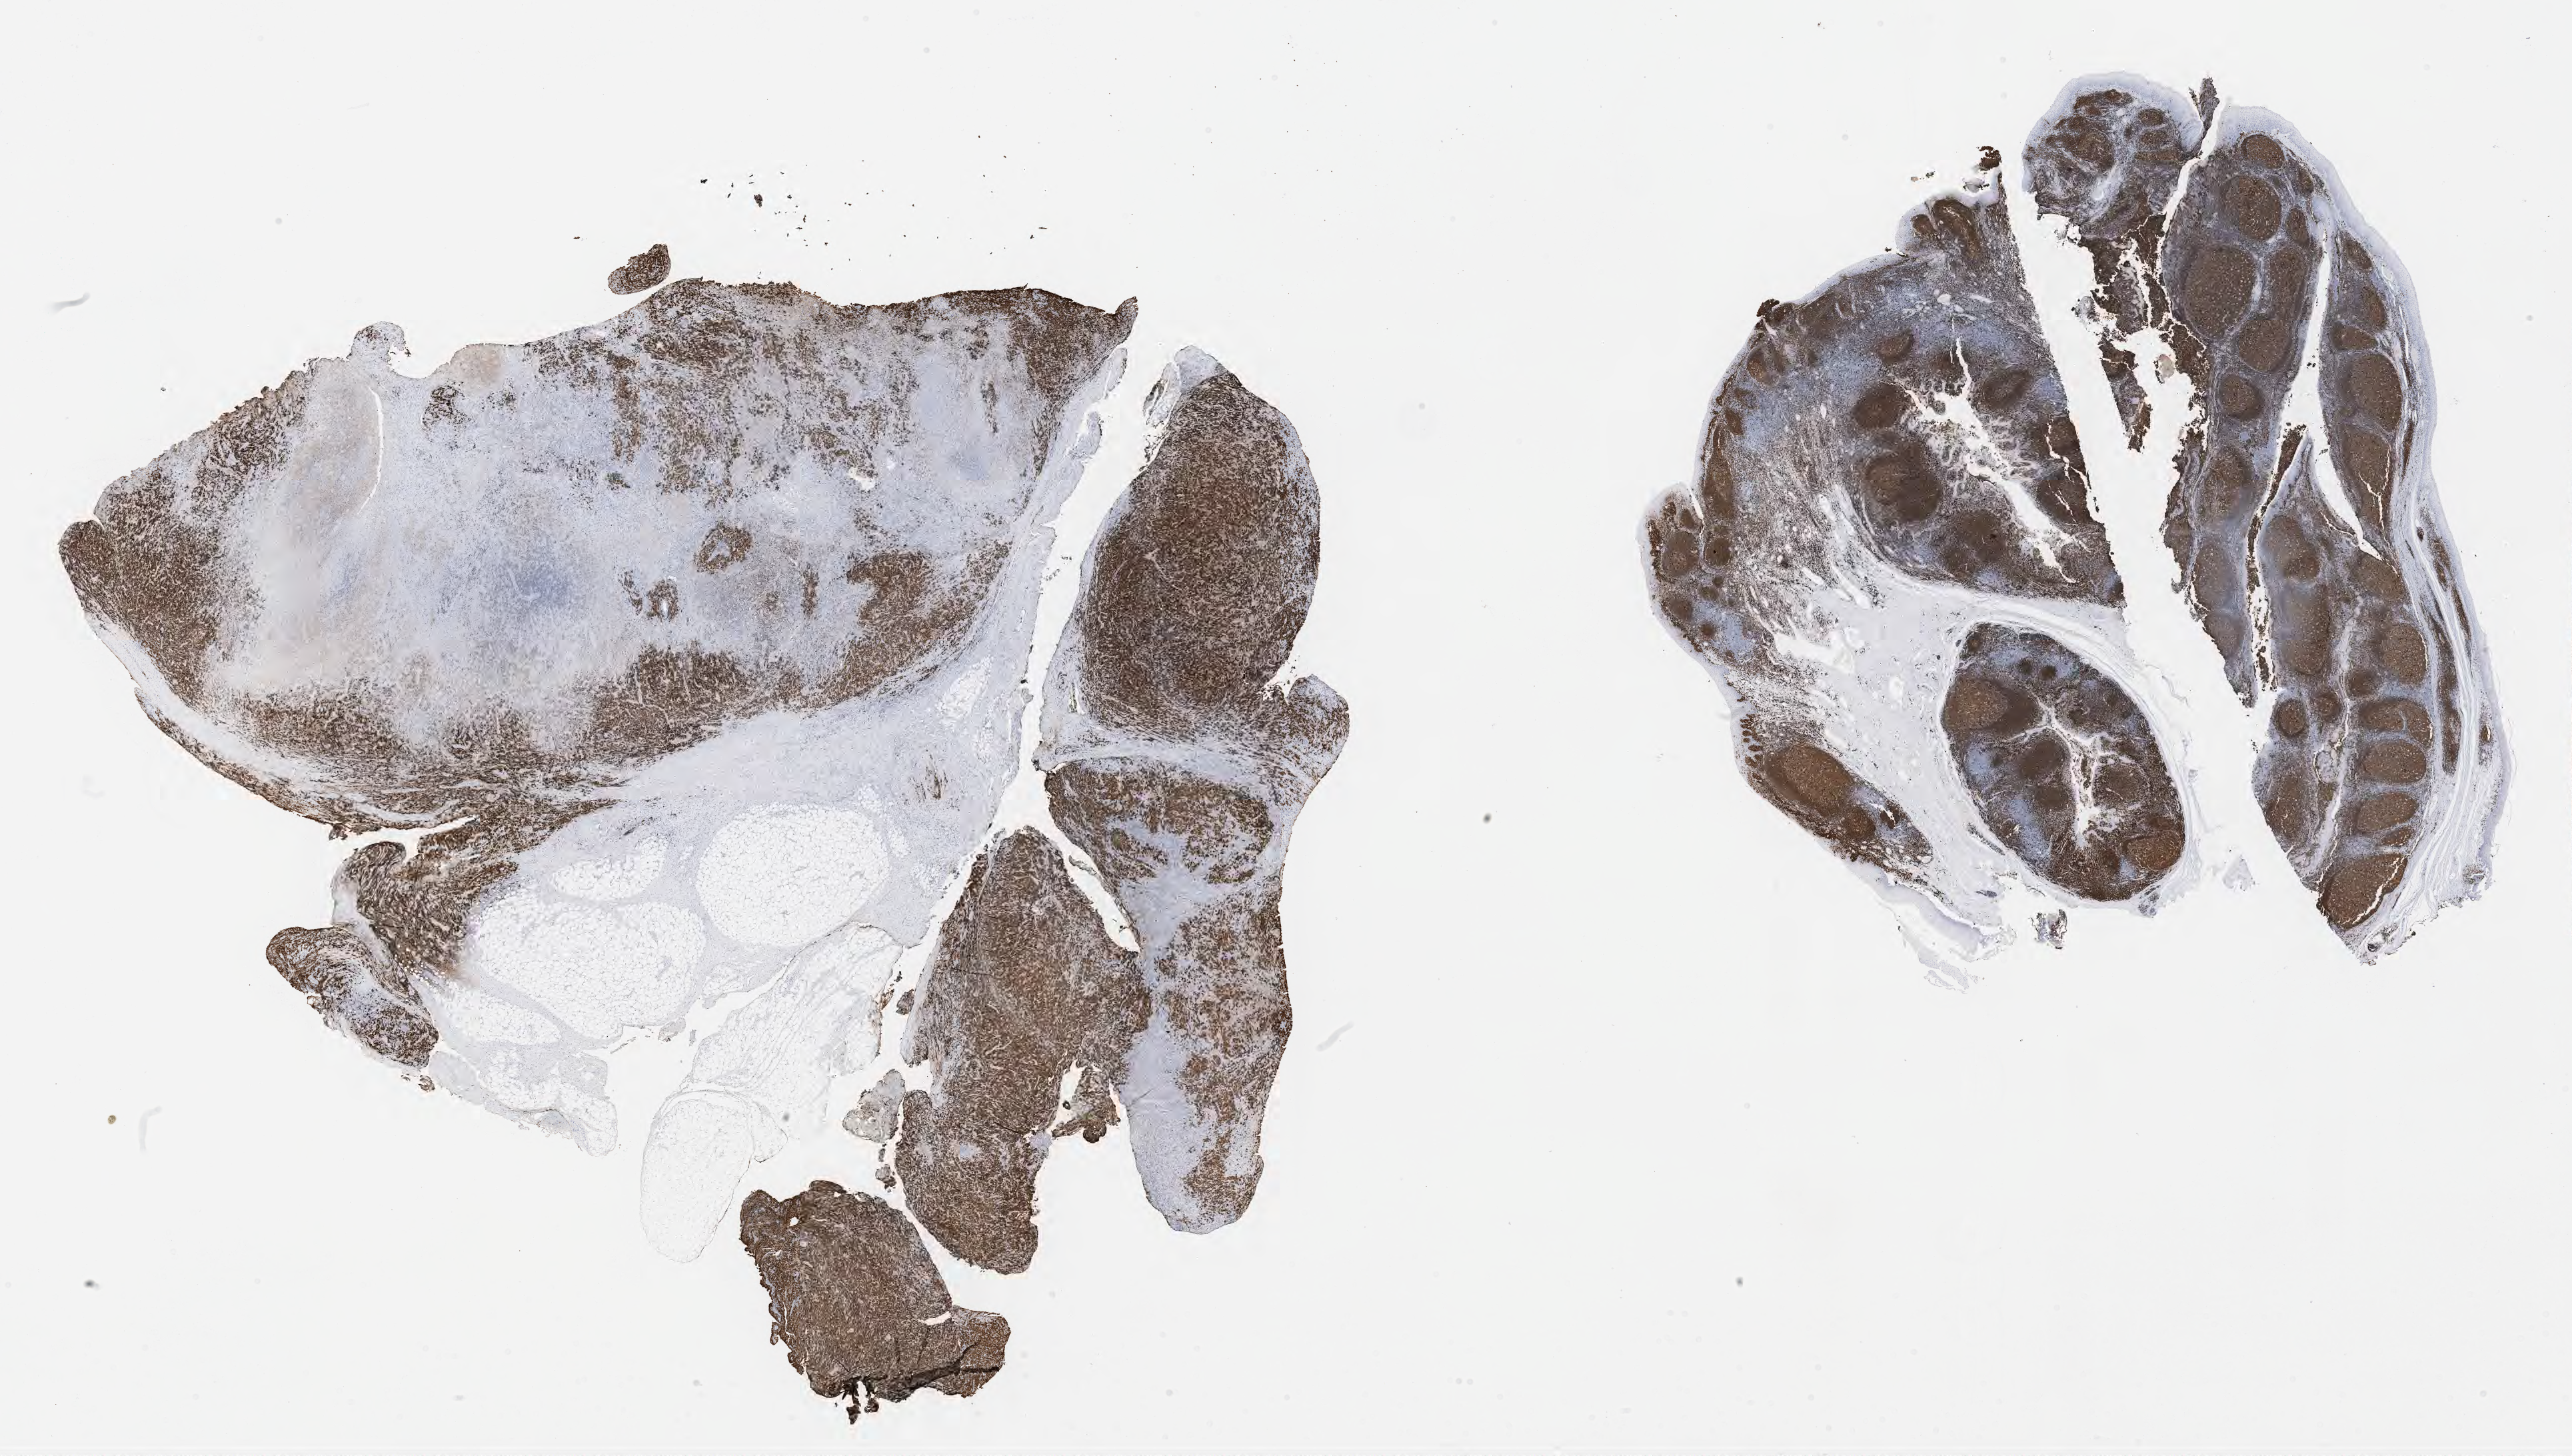
IHC for CD79a, whole-slide image, low-resolution overview of the scanned area, about 31.2 x 17.7 mm. Specimen: tumor tissue. Female patient, 46 years old.
Histologic diagnosis: Diffuse large B-cell lymphoma, NOS.